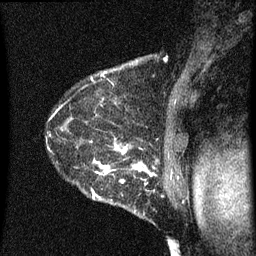
Breast MRI (dynamic contrast-enhanced), one sagittal slice. Dynamic contrast-enhanced series, image 2 of 3 at this slice position (ordered by acquisition). 1.5 T. TE 4.2 ms, TR 8 ms. 256 × 256 image matrix, field of view 180 × 180 mm. Patient: female, 54 years.
Outlined on this slice (semi-automatic segmentation, software-assisted and operator-edited):
- analysis volume of interest (the breast-tissue region the enhancement analysis was run in; not a lesion): bounding box [x1, y1, x2, y2] px = [49, 138, 164, 209]
- tumour enhancement mask (voxels above the 70 % enhancement threshold inside the analysis volume of interest): [49, 138, 156, 201]